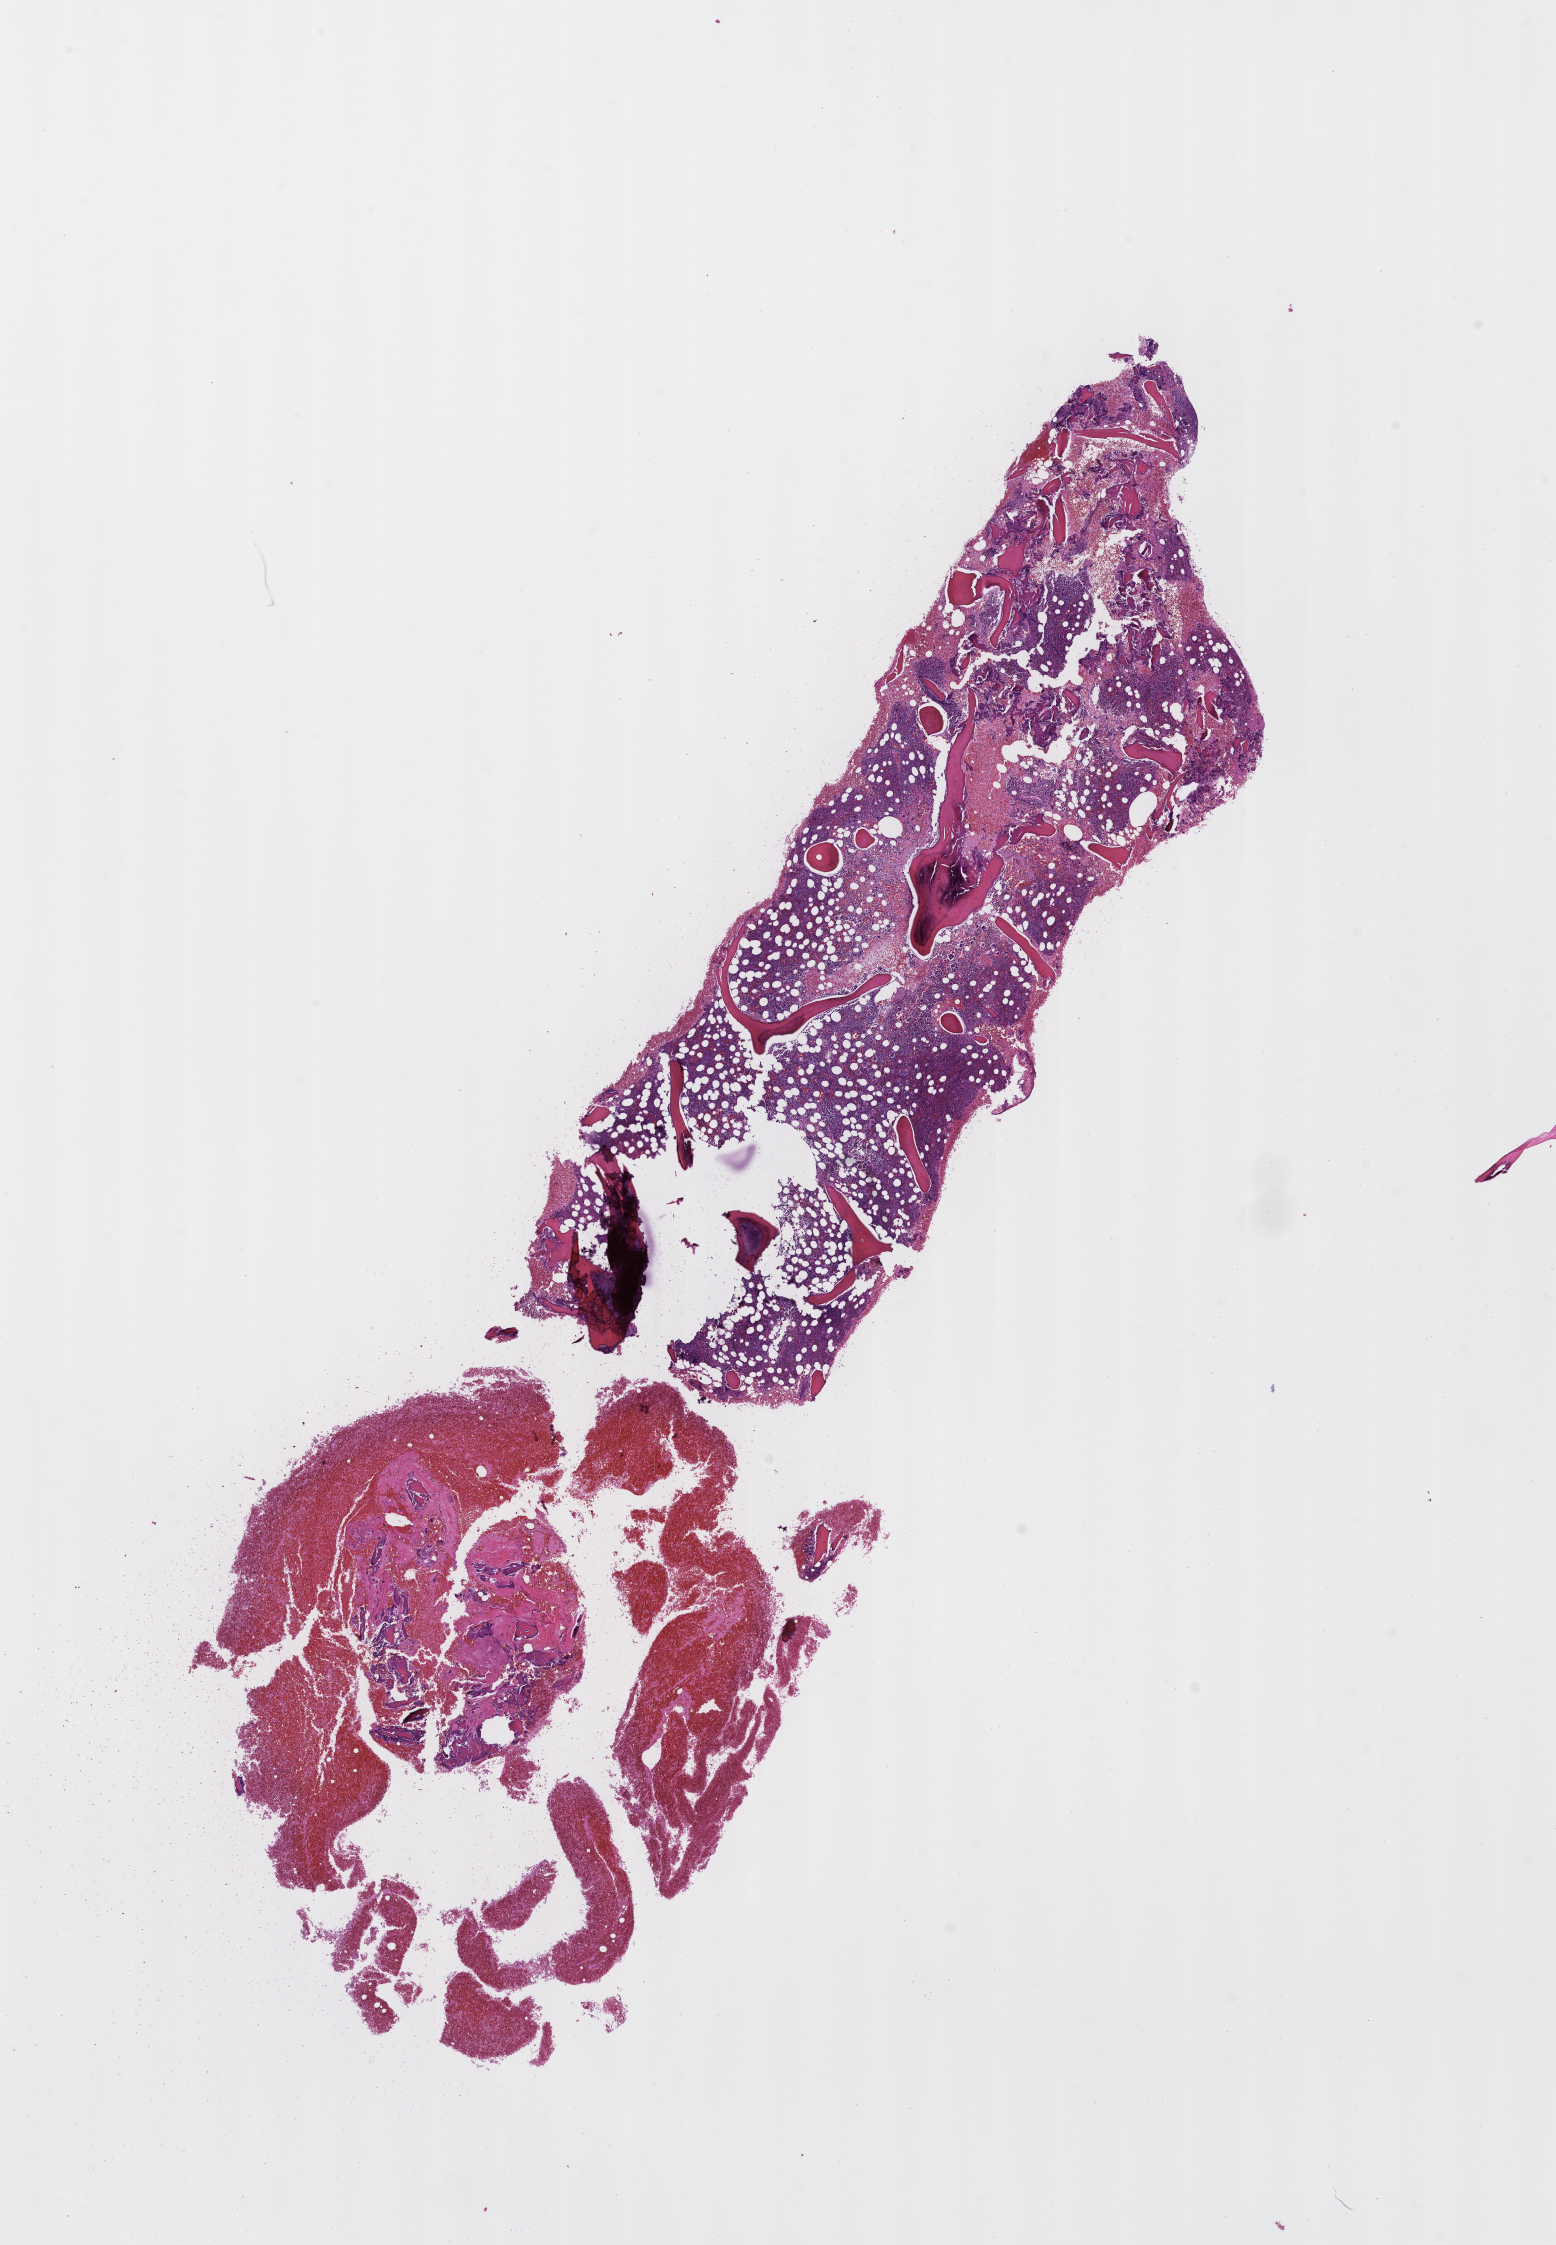
Hematoxylin and eosin (H&E) whole-slide image, low-resolution overview of the scanned area, about 12.6 x 18.1 mm, formalin-fixed, paraffin-embedded (FFPE) tissue, tissue site: bone marrow, archival tissue. Patient: female.
This section: primary tumour tissue. Diagnosis: Plasma Cell Myeloma.